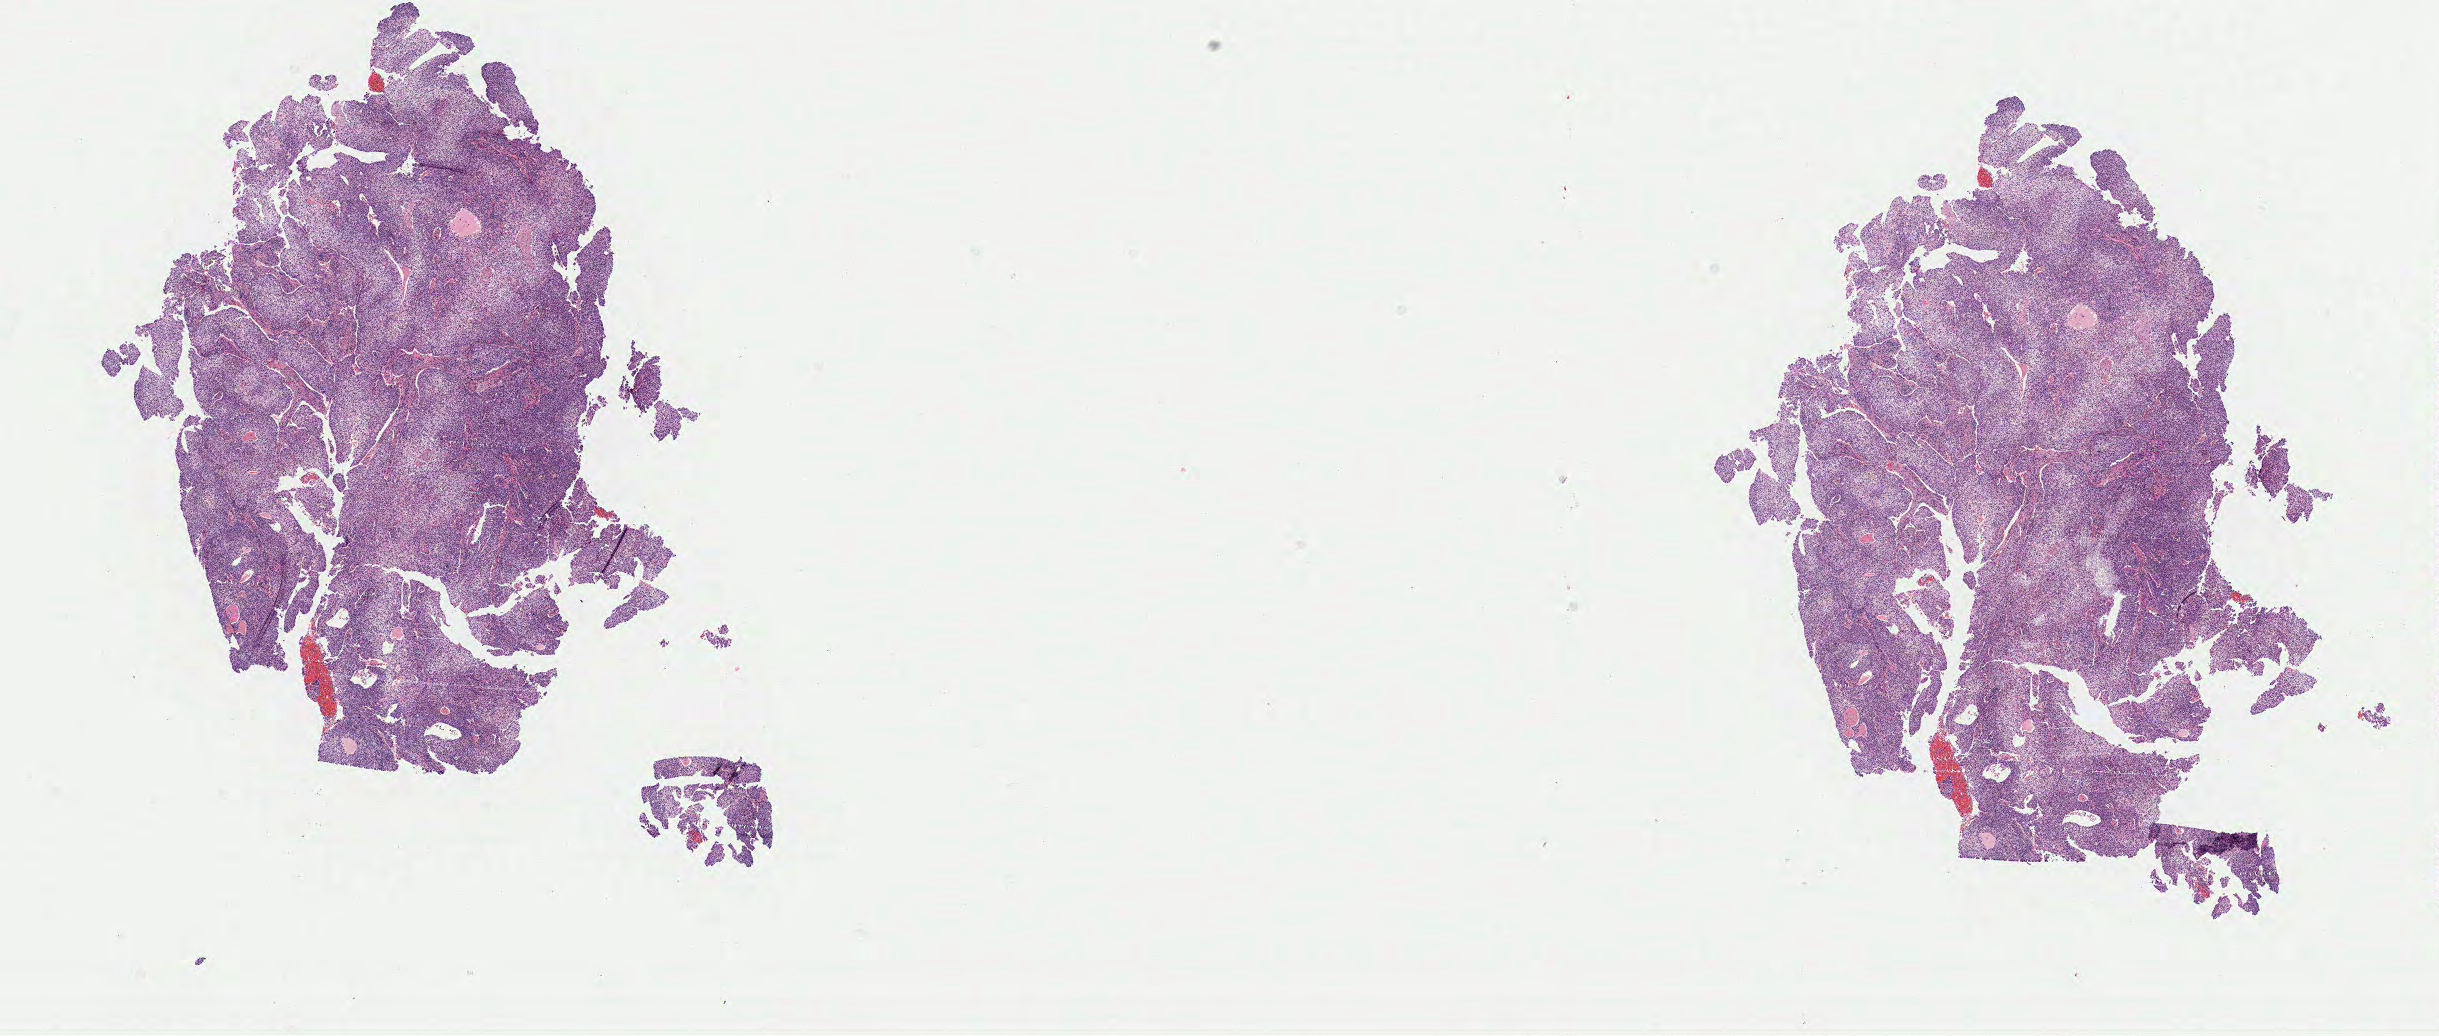
Whole-slide image, hematoxylin and eosin (H&E) stain — whole scanned area (about 19.3 x 8.2 mm) shown as a low-resolution overview, tumor tissue, anatomic site: cervix. Female patient, aged 39.
Diagnosis: Squamous cell carcinoma, large cell, nonkeratinizing, NOS.